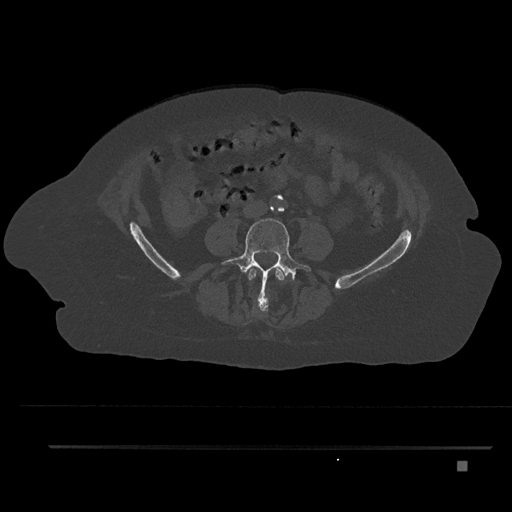
CT including the spine, one axial slice. Position 88 of 797 along the scan axis. Reconstruction kernel Br40s/3. 120 kVp. Bone window (W 1800 / L 400 HU). 0.5 mm slice thickness. 512 × 512 image matrix, field of view 437 × 437 mm. Female patient, age 76 years. From the clinical record (not read from this slice): primary cancer: lung; vertebrae with lytic lesions (as recorded): T11, L3.
Annotated regions visible in this slice (semi-automatically segmented with operator editing):
- L3 vertebra: bounding box [x1, y1, x2, y2] px = [248, 267, 285, 312]
- L4 vertebra: [221, 218, 311, 311]